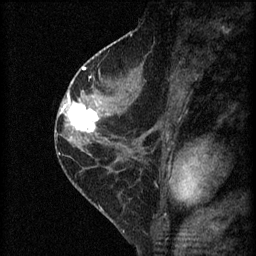
Breast MRI (dynamic contrast-enhanced), one sagittal slice. Position 32 of 60 along the scan axis. 3 images stored at this slice position (order not interpretable as contrast timing). 1.5 T. TE 4.2 ms, TR 8.2 ms. 2 mm slice thickness. 256 × 256 image matrix, field of view 180 × 180 mm. Female patient, age 45 years.
Annotated regions visible in this slice (semi-automatic segmentation, software-assisted and operator-edited):
- analysis volume of interest (the breast-tissue region the enhancement analysis was run in; not a lesion): bounding box [x1, y1, x2, y2] px = [62, 98, 104, 139]
- tumour enhancement mask (voxels above the 70 % enhancement threshold inside the analysis volume of interest): [62, 98, 100, 133]